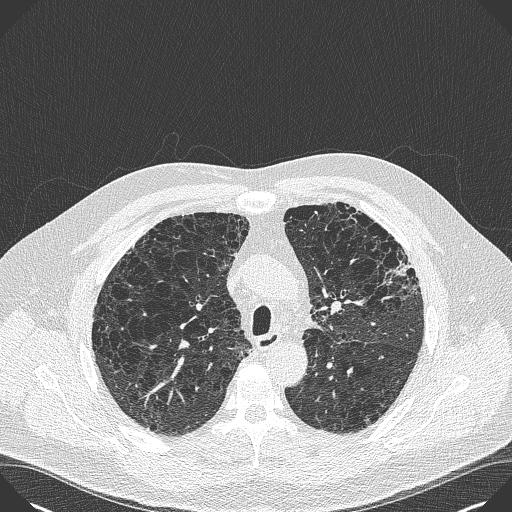
Low-dose screening chest CT, axial slice. Baseline screening round. Lung window (W 1500 / L -600 HU). Lung (sharp) reconstruction kernel (B50f). 512 × 512 image matrix. Male, age 59 years at enrolment. Current smoker at enrolment.
• Lesion marked by an expert reader, bounding box [x1, y1, x2, y2] px = [375, 239, 427, 290].
• No non-calcified nodule or mass ≥4 mm was recorded by the screening reader at this exam.
• Lung cancer was diagnosed 909 days after this screen (after the third annual screen): bronchiolo-alveolar carcinoma, mixed mucinous and non-mucinous, left upper lobe, stage IA (AJCC 6th edition), 20 mm at pathology.